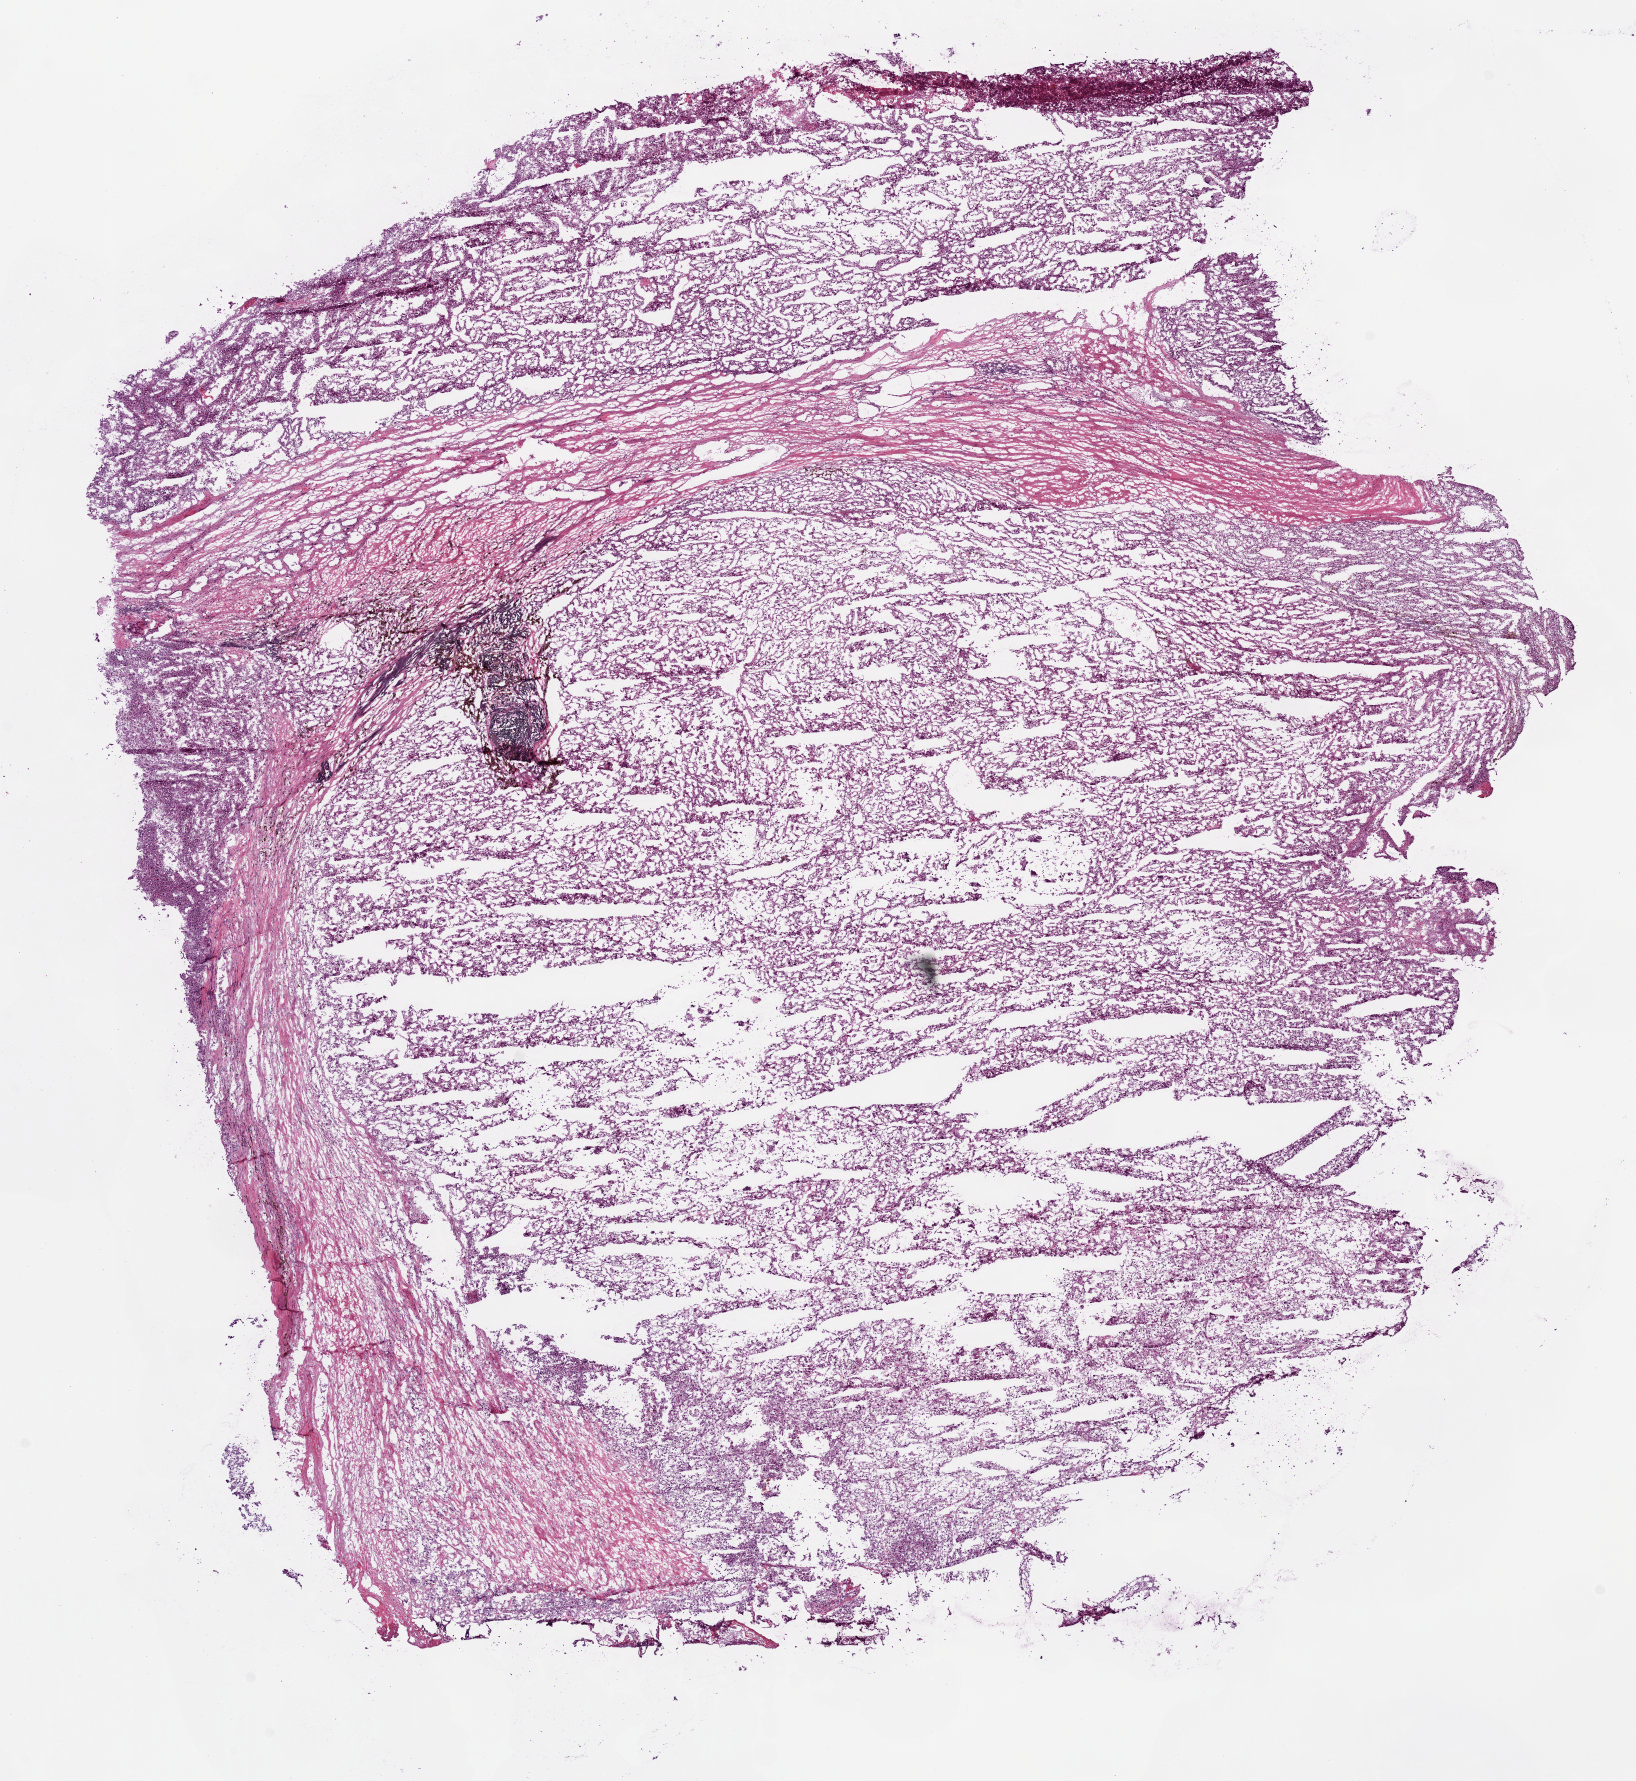
Hematoxylin and eosin (H&E) stained whole-slide image, whole scanned area (about 13.1 x 14.3 mm, from a 5x scan) shown as a low-resolution overview. Frozen section. Kidney, primary tumour sample. Female patient; age at initial diagnosis 59 years. Histologic grade: G4 (undifferentiated). Pathologist review of this section (percent, as recorded): tumour cells 85%, tumour nuclei 85%, normal cells 0%, stromal cells 15%, necrosis 0%.
Diagnosis: Clear cell adenocarcinoma, NOS. AJCC pathologic stage: III (6th edition).